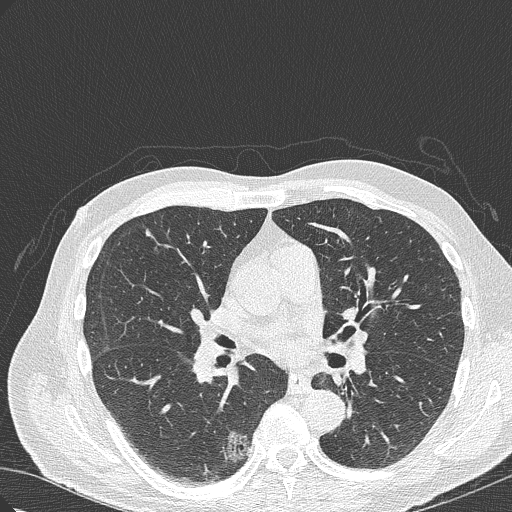
Chest CT (low-dose screening protocol), one axial image, first (baseline) screen, lung window (W 1500 / L -600 HU), 1 mm slice thickness, lung (sharp) reconstruction kernel (B50f), slice 146 of 322 in the series, 512 × 512 image matrix. Male participant, aged 70 years at enrolment. Current smoker at enrolment.
Lesion marked by an expert reader, bounding box (x1, y1, x2, y2) in pixels: (198, 420, 261, 480). The screening reader recorded 4 non-calcified nodules or masses ≥4 mm on this exam; which of them this box marks is not recorded. Official screen result: positive, change unspecified: nodule(s) >= 4 mm or enlarging nodule(s), mass(es), or other non-specific abnormalities suspicious for lung cancer. Participant outcome: lung cancer diagnosed 978 days after this screen — bronchiolo-alveolar adenocarcinoma, NOS, right lower lobe, poorly differentiated (G3), stage IB (AJCC 6th edition), 30 mm at pathology.